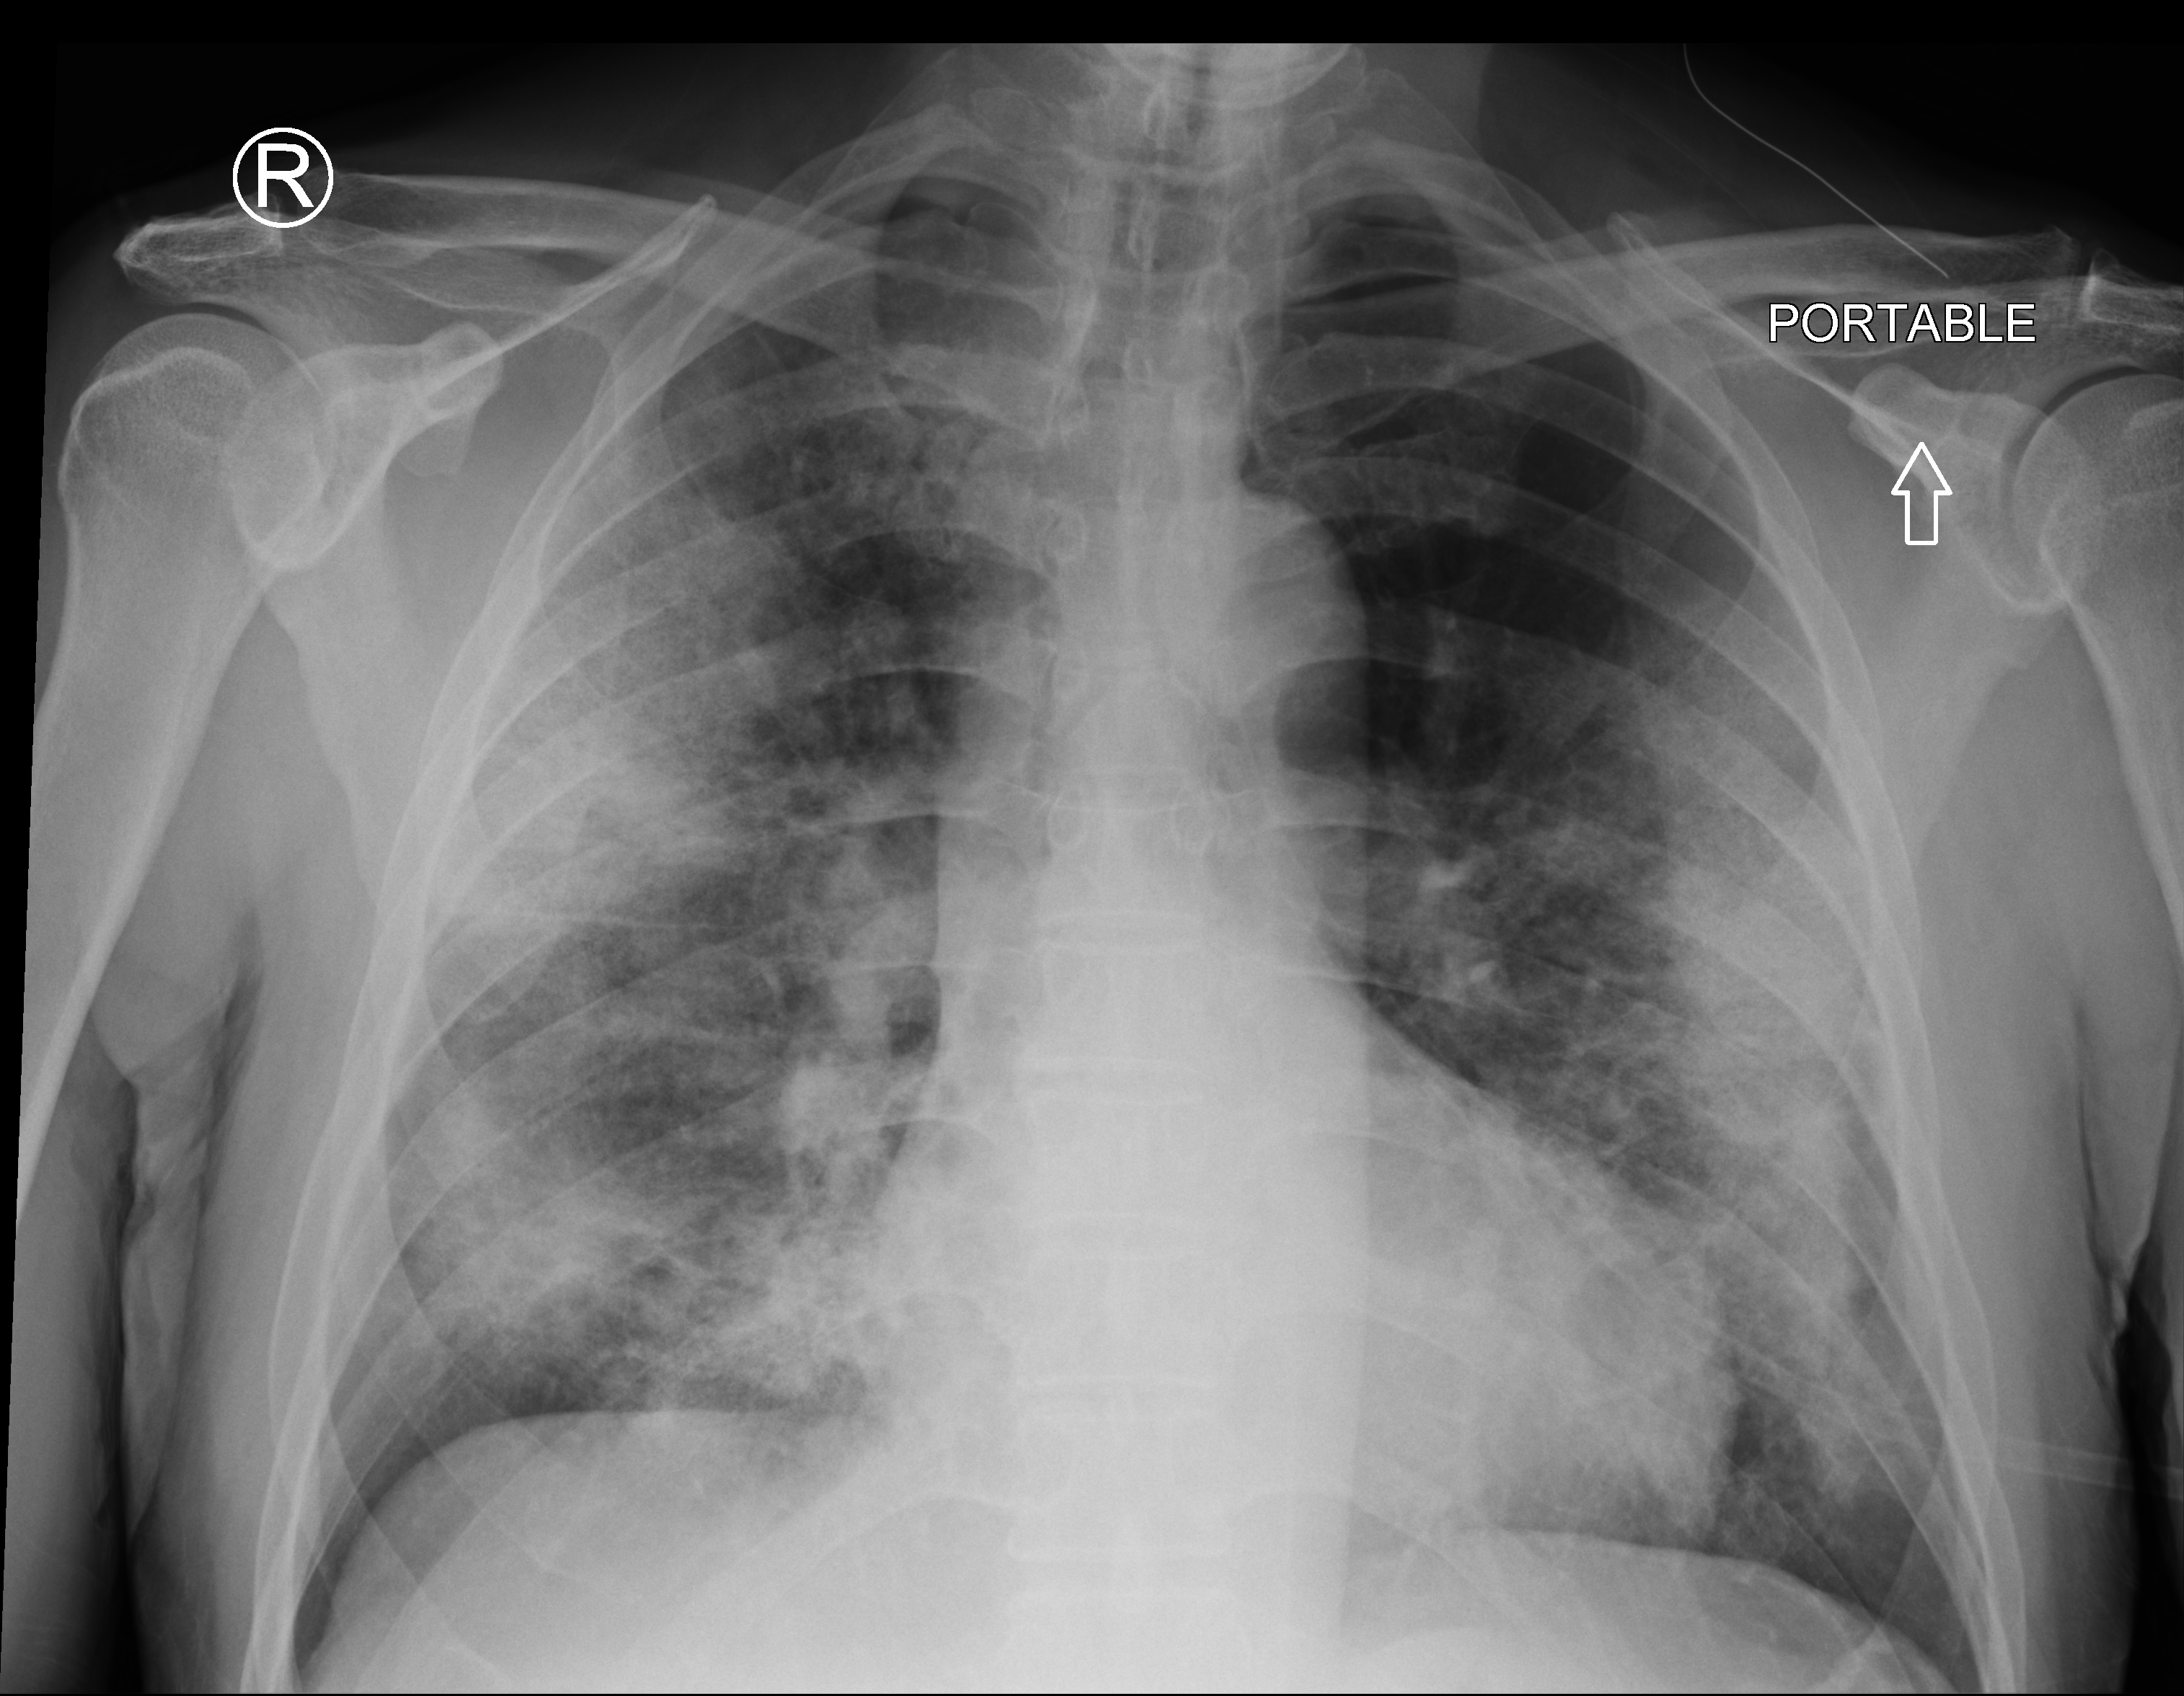
Bedside chest radiograph (computed radiography), anteroposterior (AP) projection. Patient hospitalised with COVID-19; male, aged 60–74 years.
Hospital-stay facts (about this admission, not read from this image; timing relative to this image not recorded): admitted to intensive care during this hospital stay: no; diabetes (admission record): yes; mechanically ventilated during this hospital stay: no.